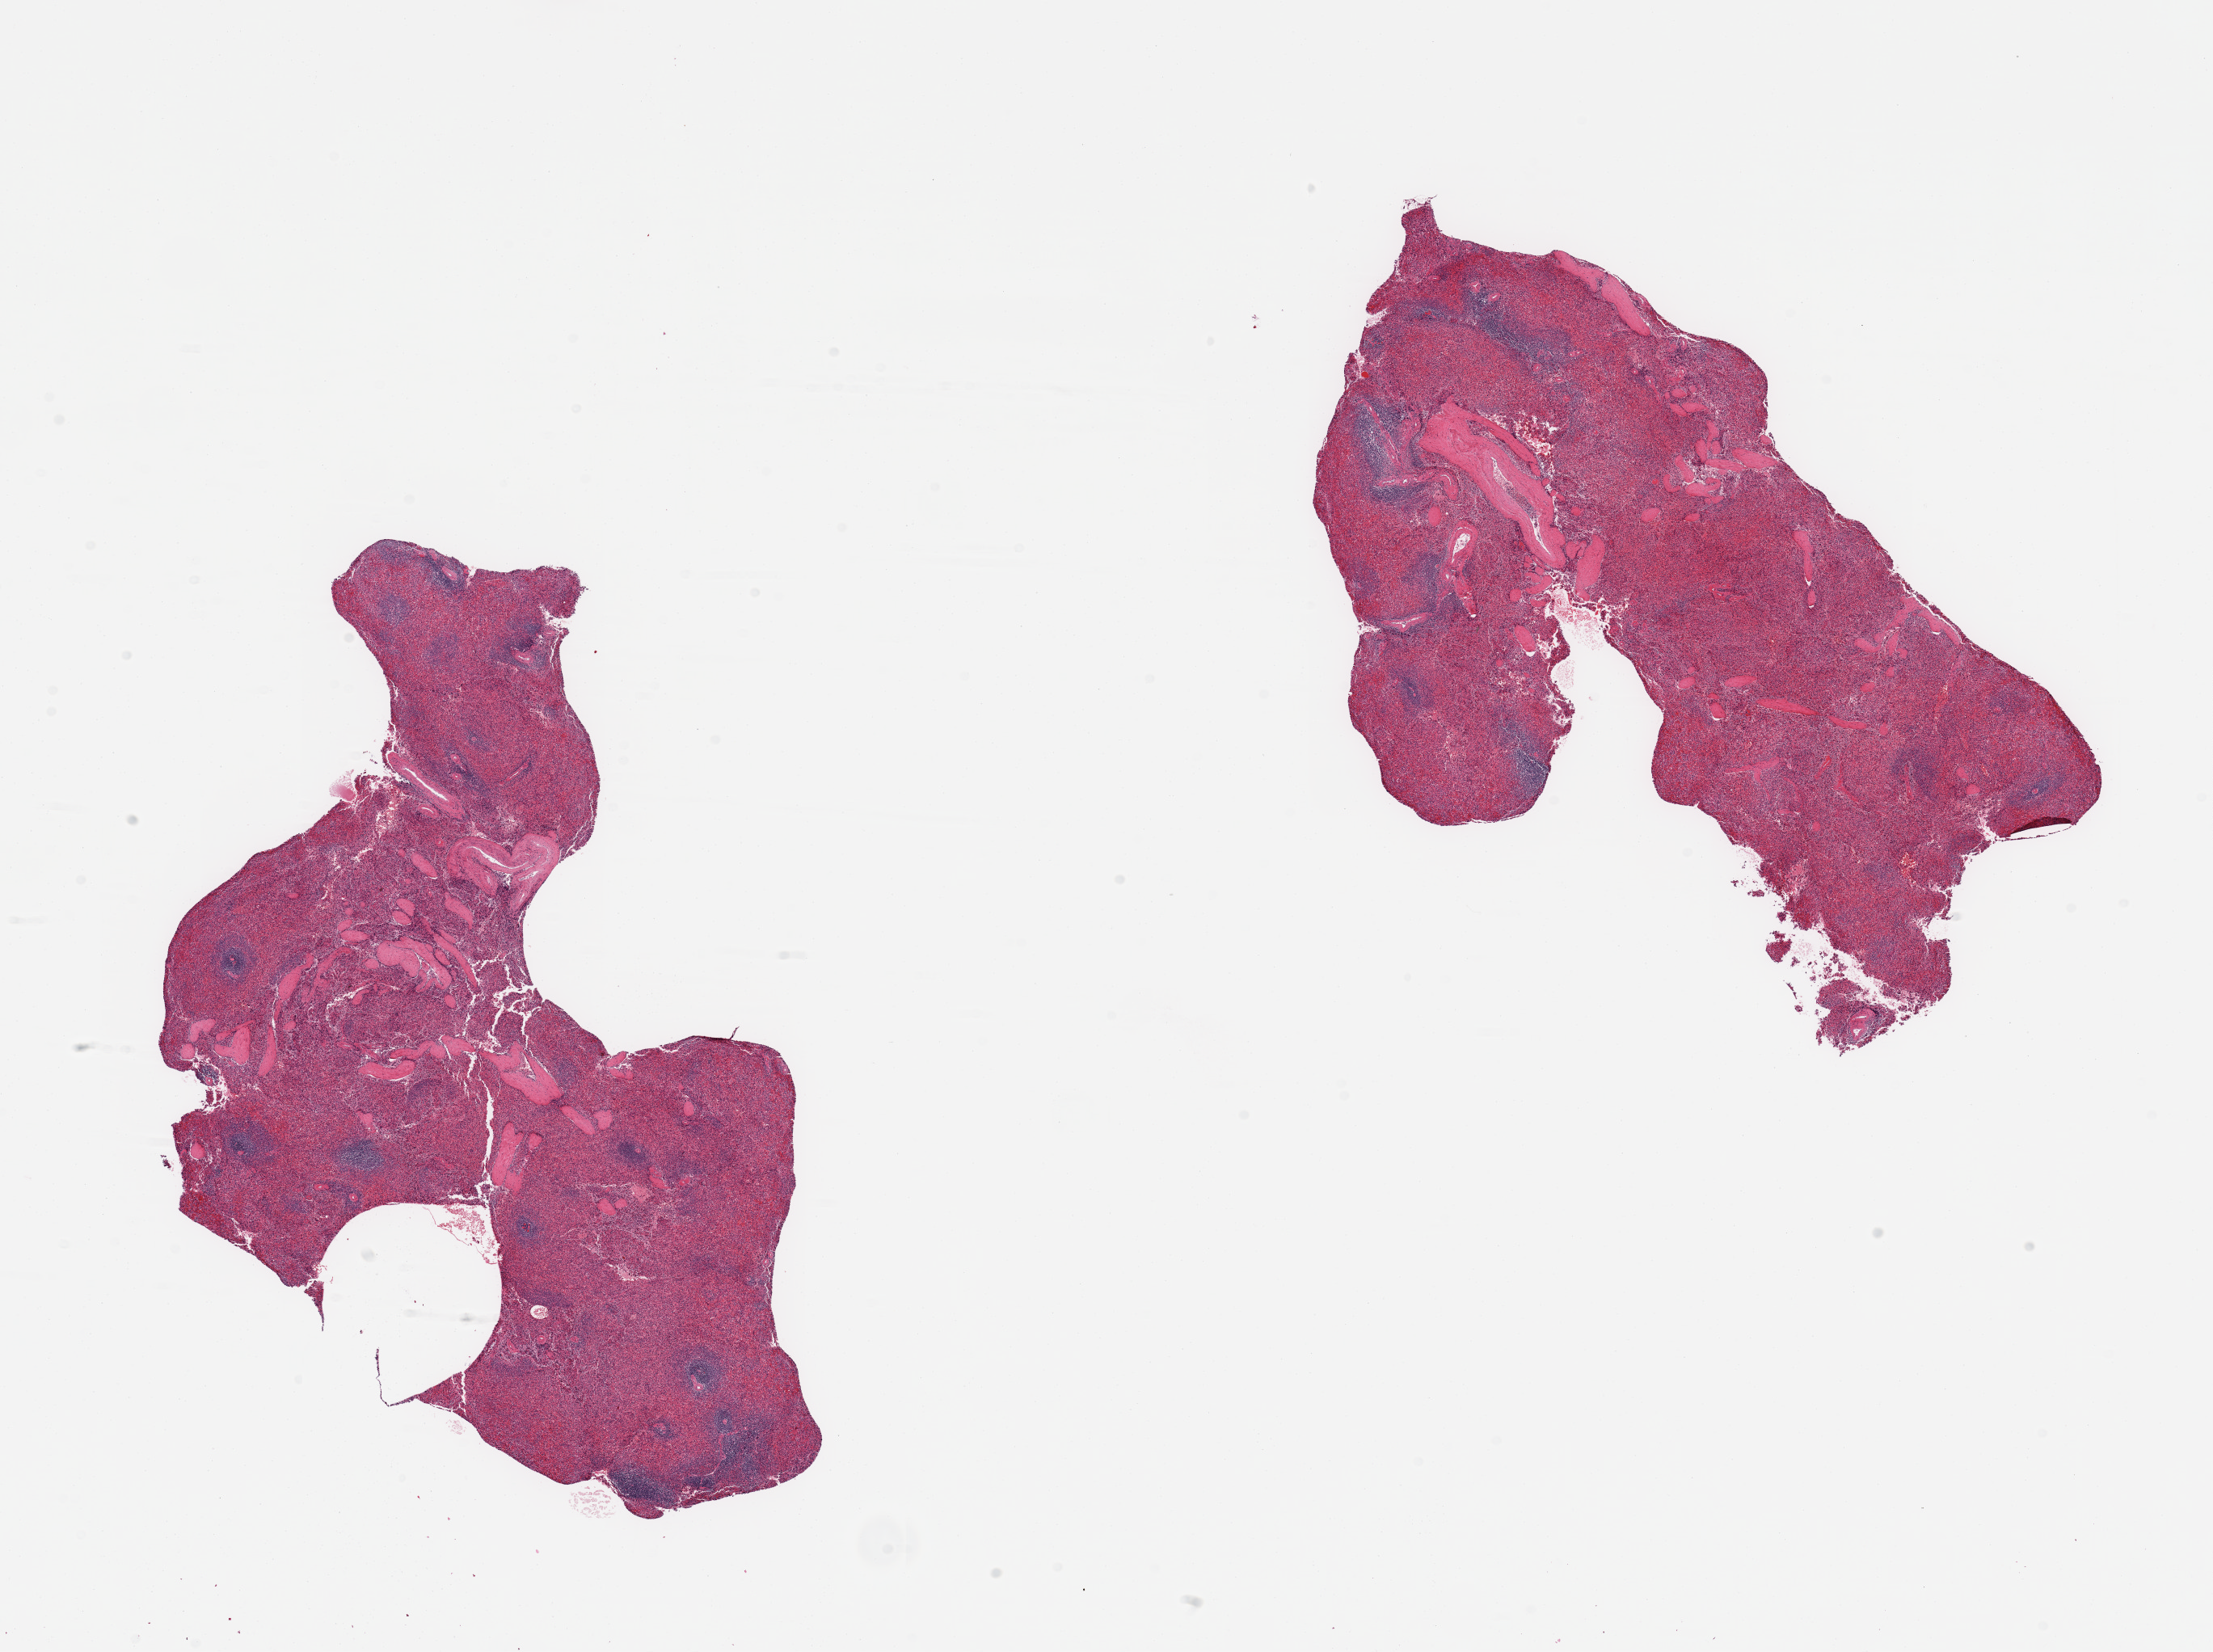
Whole-slide image, haematoxylin and eosin stain, a low-resolution overview of the entire scanned area, about 21.7 x 16.2 mm. PAXgene-fixed paraffin-embedded (PFPE) section. Section of spleen (target tissue). Donor tissue sample. Donor: male.
Pathologist's review note for this sample: 2 pieces; congestion.